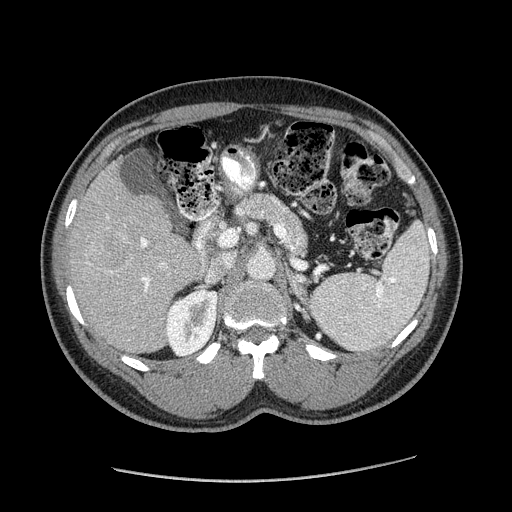
Contrast-enhanced abdominal CT (liver protocol), one axial slice. Slice 99 of 182 in the series (ordered by position). 120 kVp. Soft-tissue window (W 400 / L 40 HU). 2.5 mm slice thickness. 512 × 512 image matrix, field of view 400 × 400 mm. From the clinical record (not read from this slice): diagnosis: hepatocellular carcinoma (patient treated with transarterial chemoembolisation; whether this scan precedes or follows treatment is not stated here); TNM stage (as recorded): Stage-I; Child-Pugh class: A; tumour differentiation: well differentiated; tumour nodularity: uninodular.
Outlined on this slice (semi-automatic segmentation, software-assisted and operator-edited):
- liver parenchyma outside the tumour (the mass and vessels are separate outlines, so this box may not span the whole liver): box from (x=68, y=158) to (x=206, y=352) px
- mass: (x=83, y=228)–(x=134, y=274)
- liver vessels: (x=106, y=215)–(x=166, y=292)